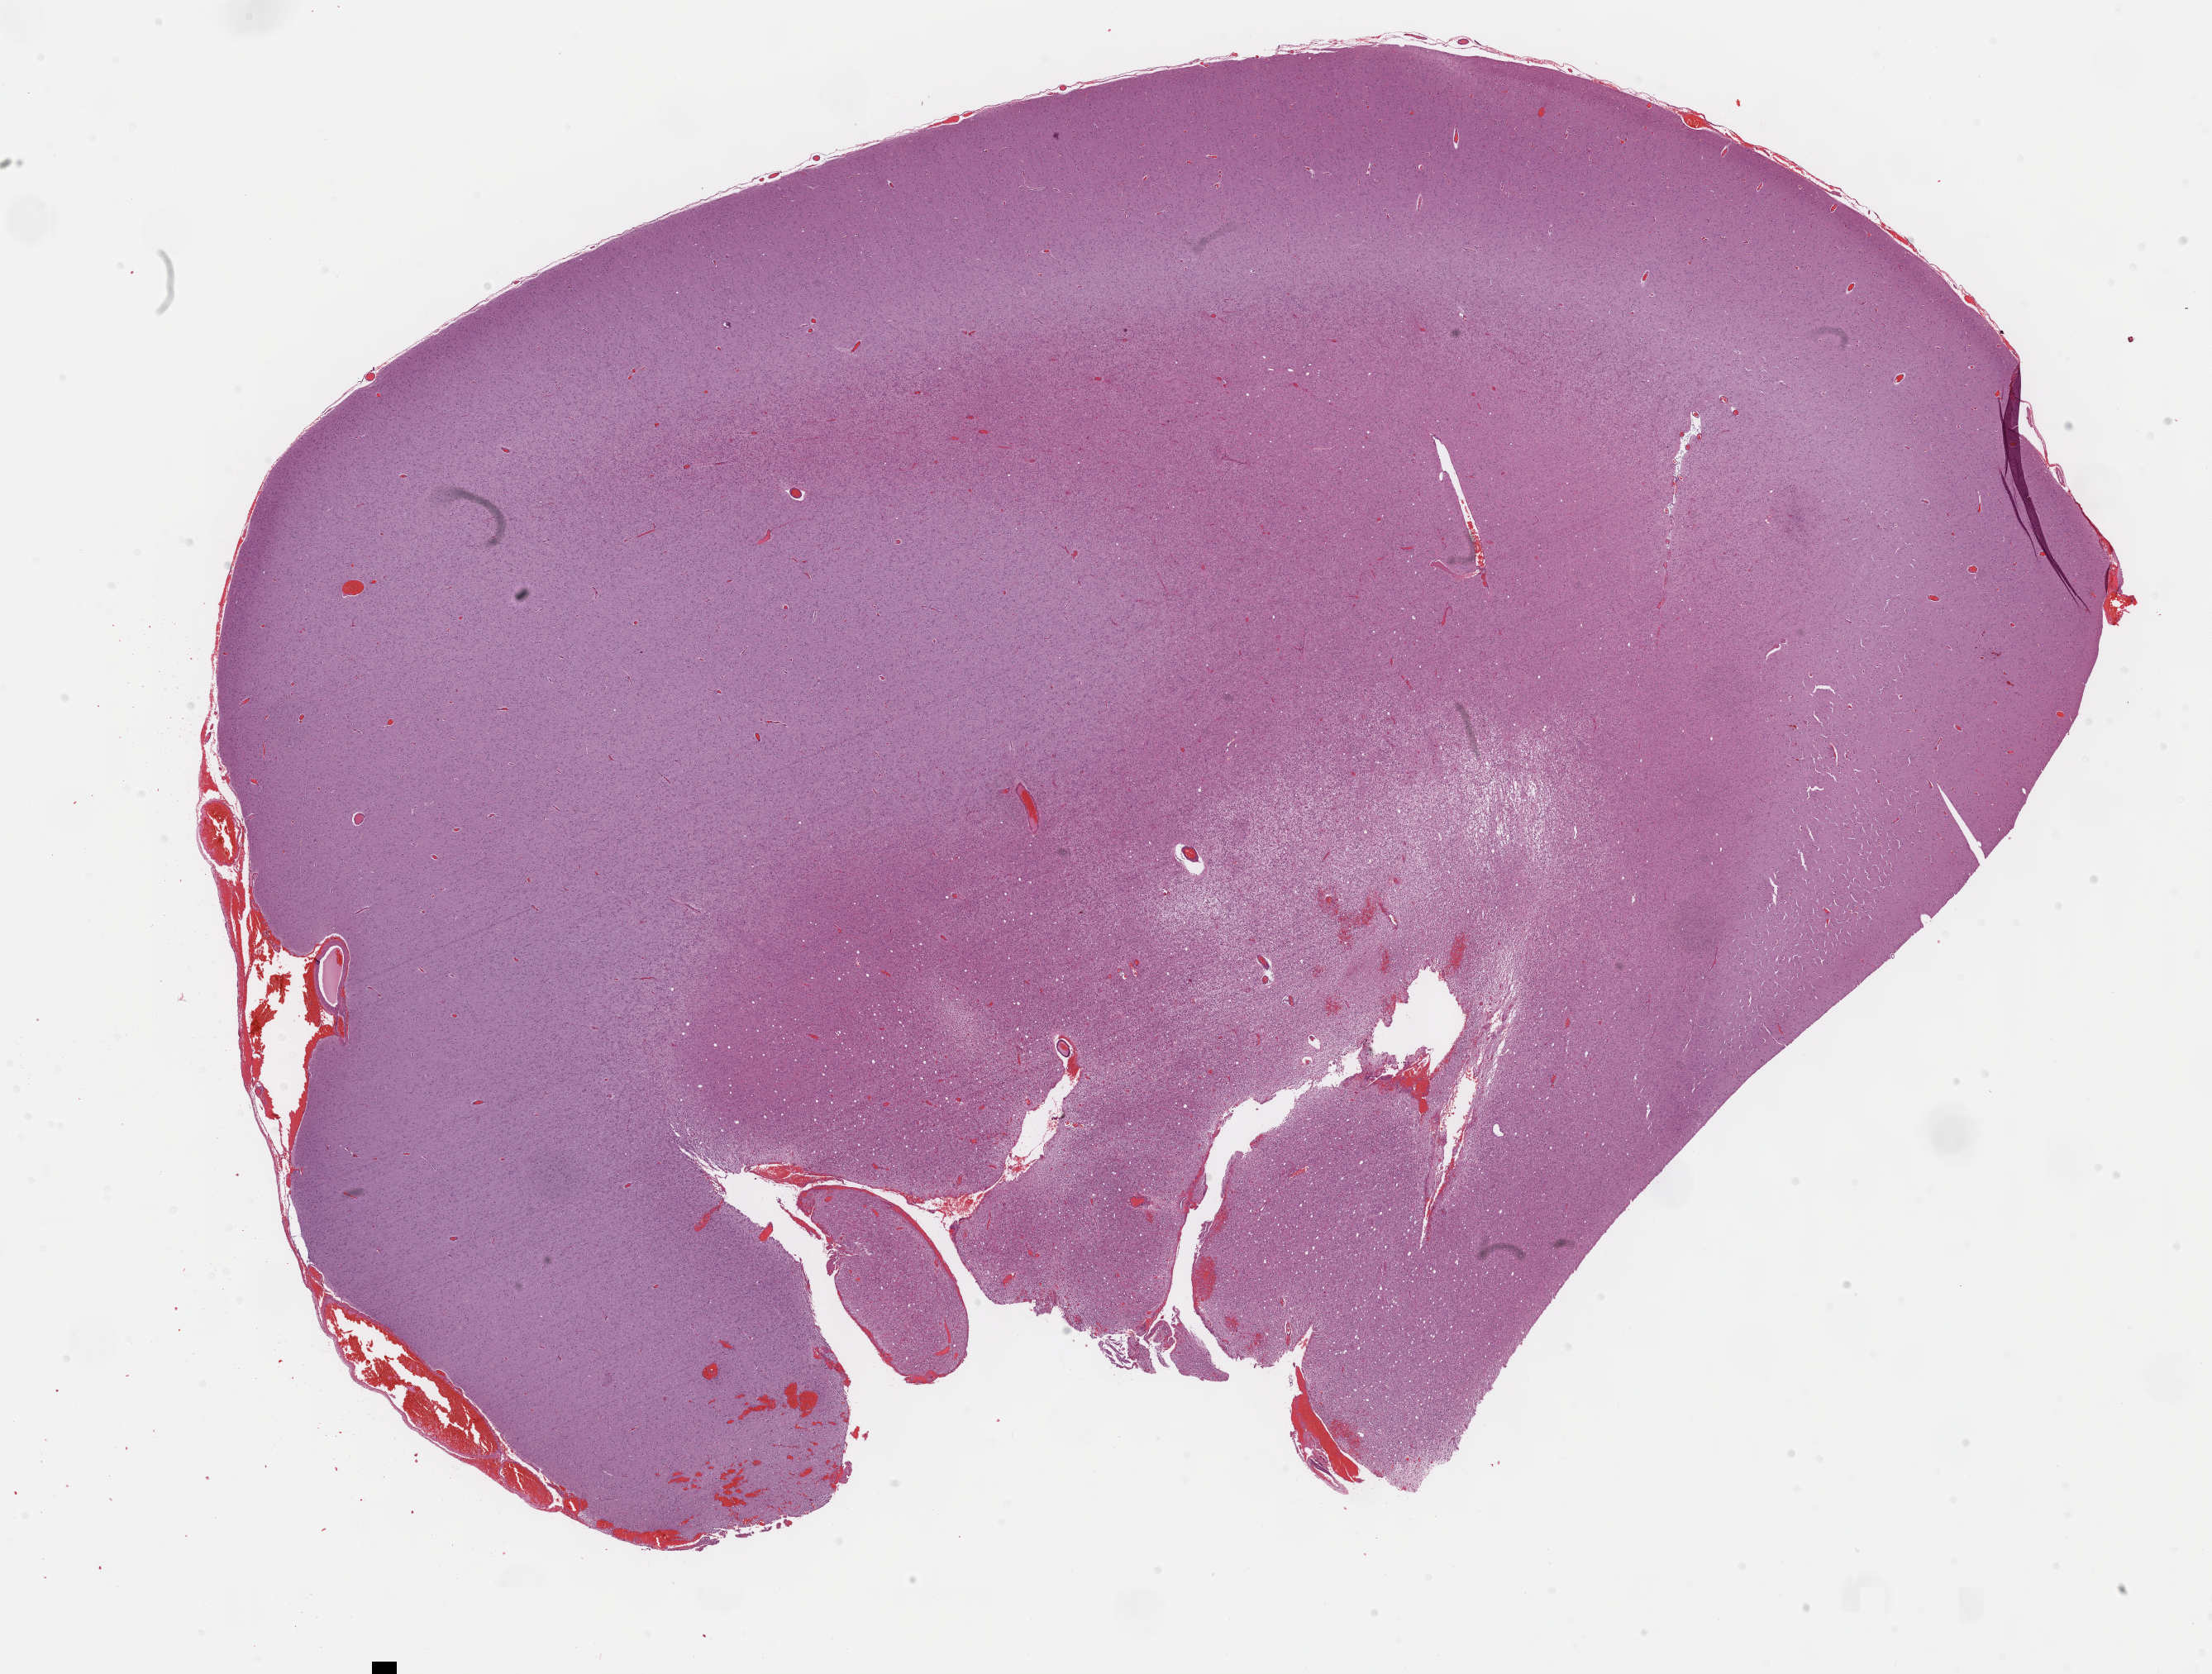
Digitized H&E tissue section (whole slide), shown as a low-resolution overview of the whole scanned area (about 21.6 x 16.4 mm), FFPE section, brain, primary tumour sample. Patient: male, age at initial diagnosis 33 years.
Histologic diagnosis: Oligodendroglioma, NOS.